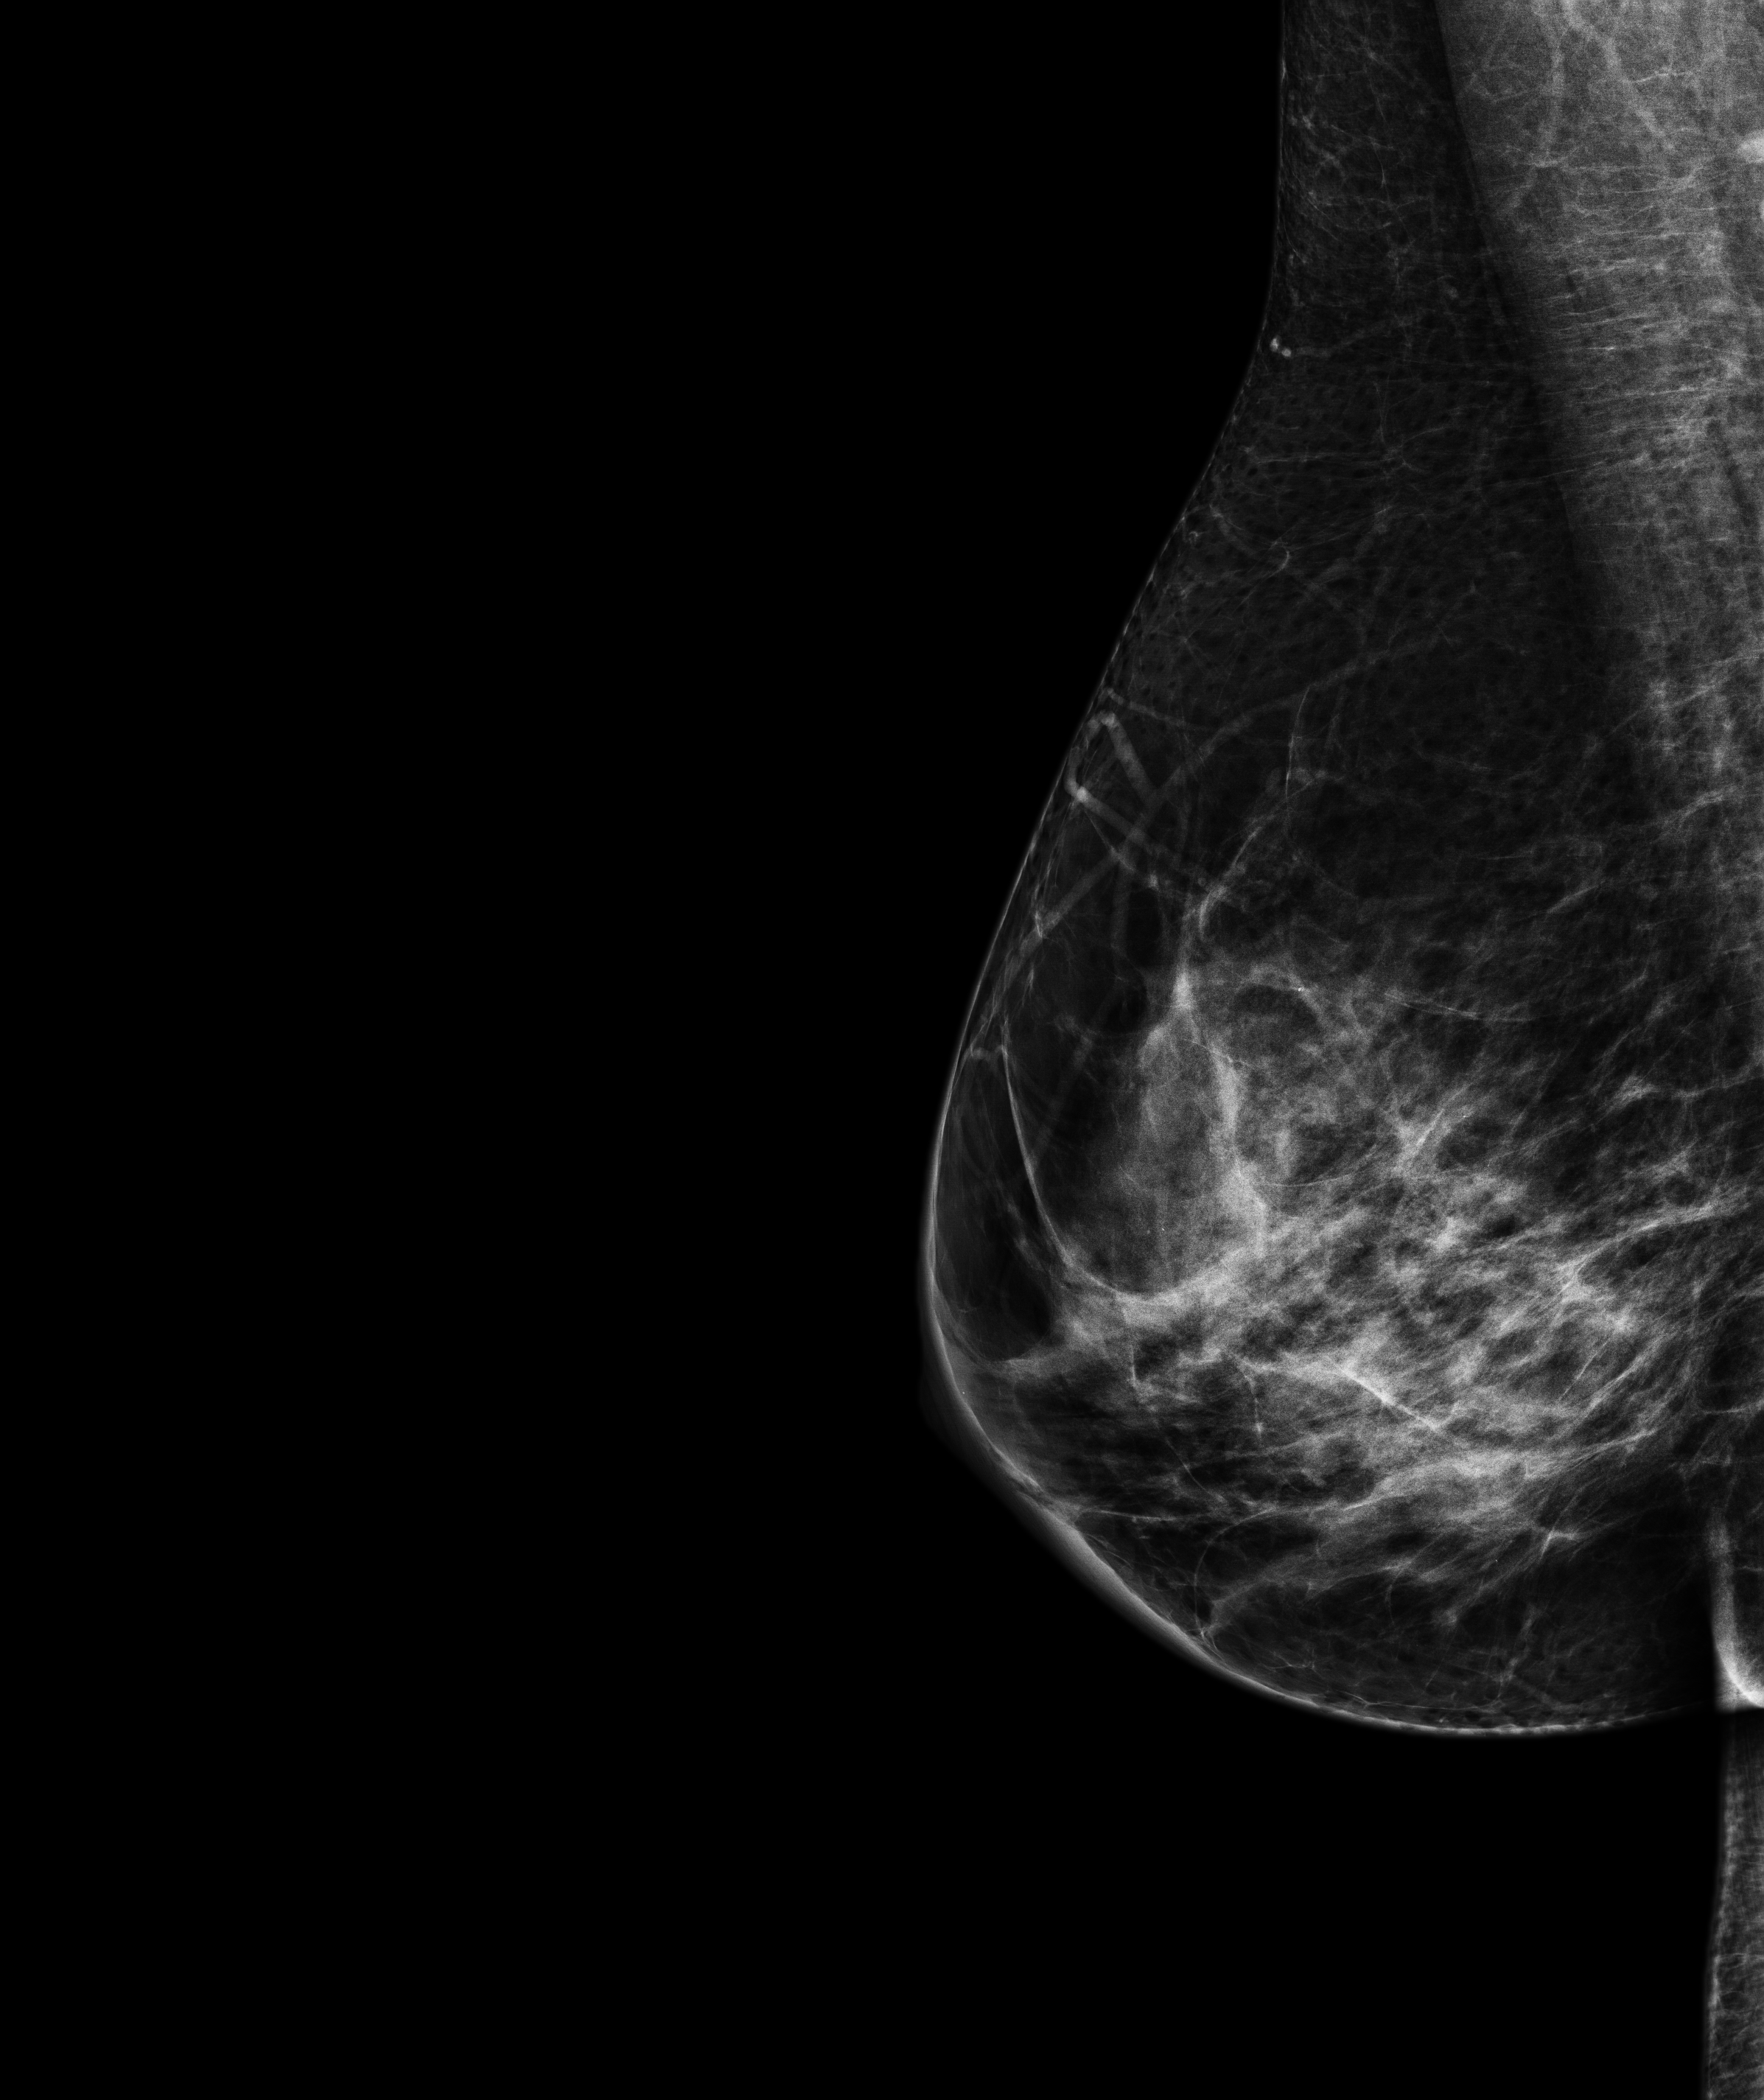
Annual screening mammography examination, system: Senographe Pristina. Patient aged 45 years (female).
Image type: full-field digital mammogram. Breast: right. Projection: medio-lateral oblique projection.